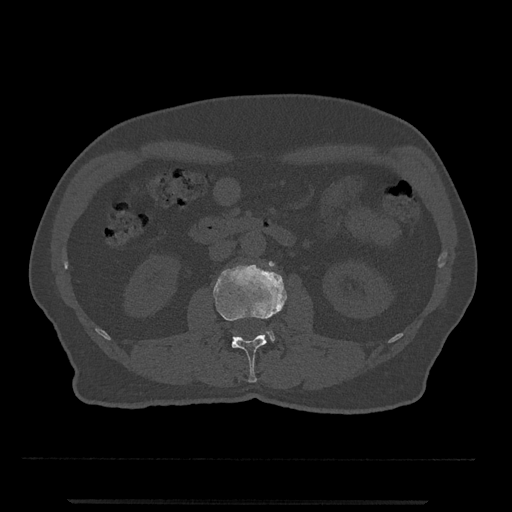
CT including the spine, one axial slice. Position 252 of 797 along the scan axis. Reconstruction kernel Br40s/3. Bone window (W 1800 / L 400 HU). 0.5 mm slice thickness. 512 × 512 image matrix. Patient: male, 63 years. Case-level facts recorded for this patient, not image findings: primary cancer: prostate.
Outlined on this slice (semi-automatically segmented with operator editing):
- L2 vertebra: box from (x=214, y=264) to (x=287, y=383) px
- L3 vertebra: (x=266, y=331)–(x=275, y=341)